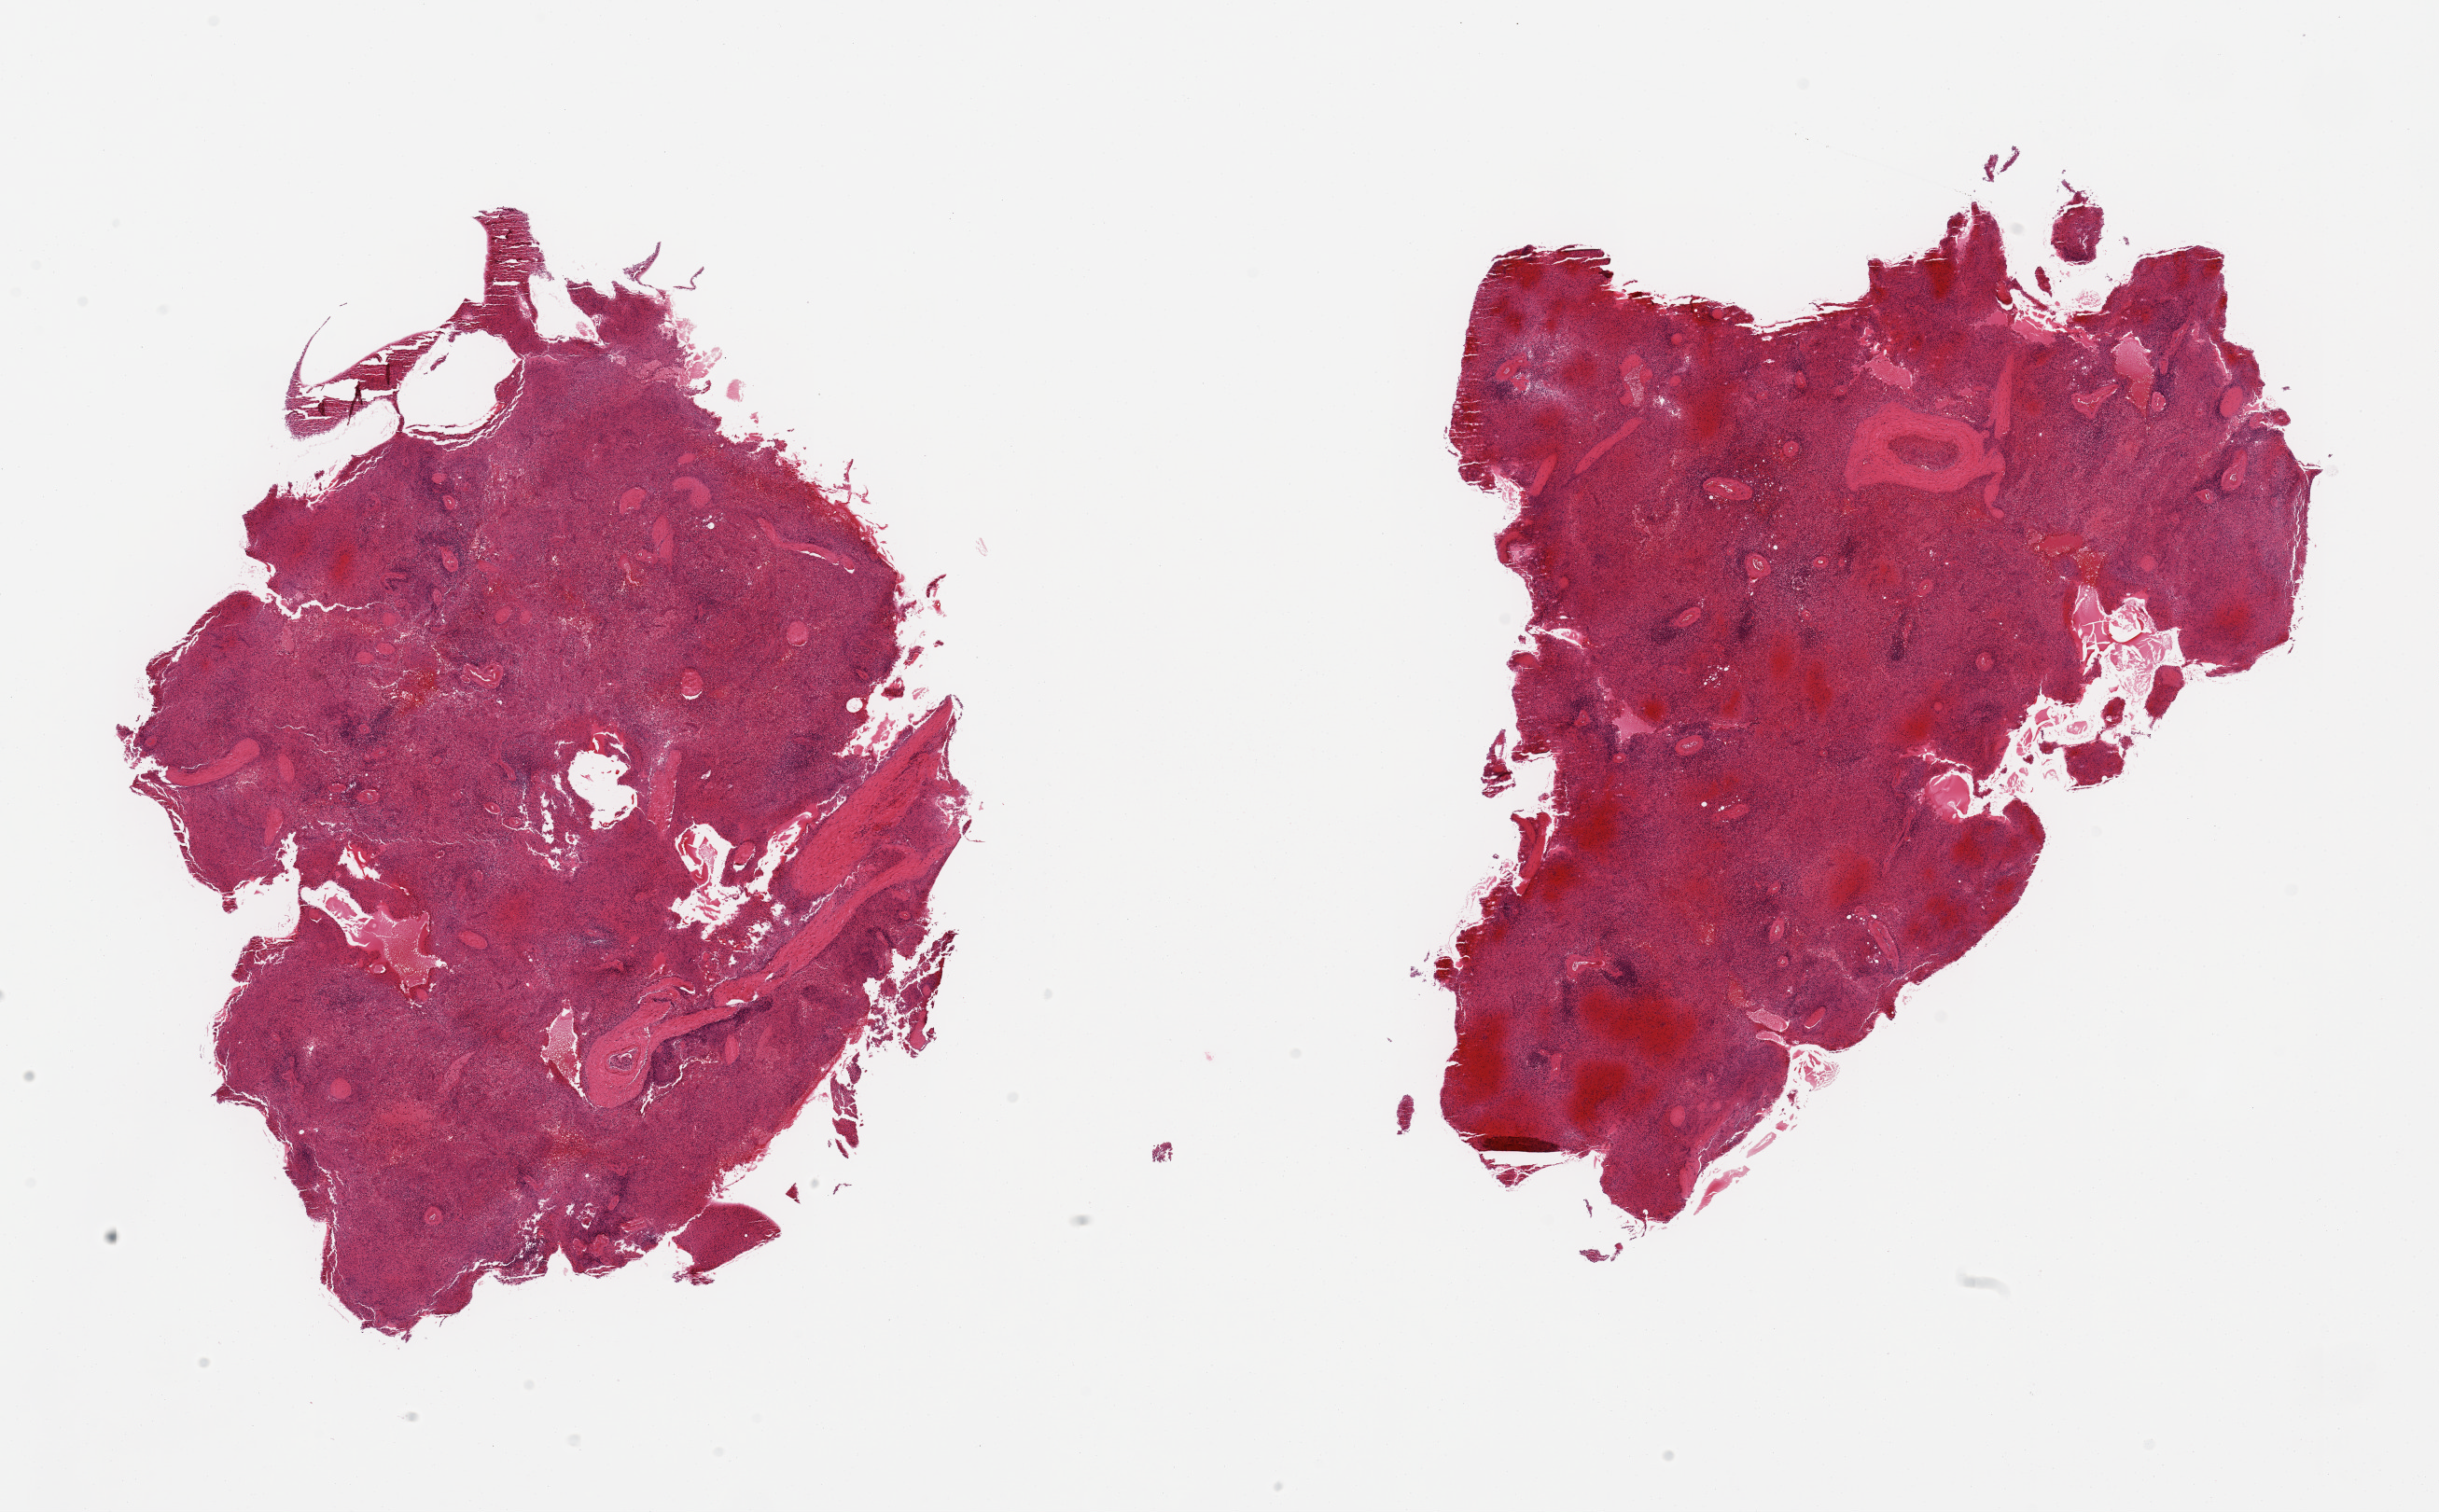
Hematoxylin and eosin (H&E) whole-slide image — shown as a low-resolution overview of the whole scanned area (about 20.7 x 12.8 mm, from a 20x scan), PAXgene-fixed, paraffin-embedded tissue, section of spleen (target tissue), donor tissue sample. Donor sex: male.
Review note (as recorded): 2 pieces; marked congestion.